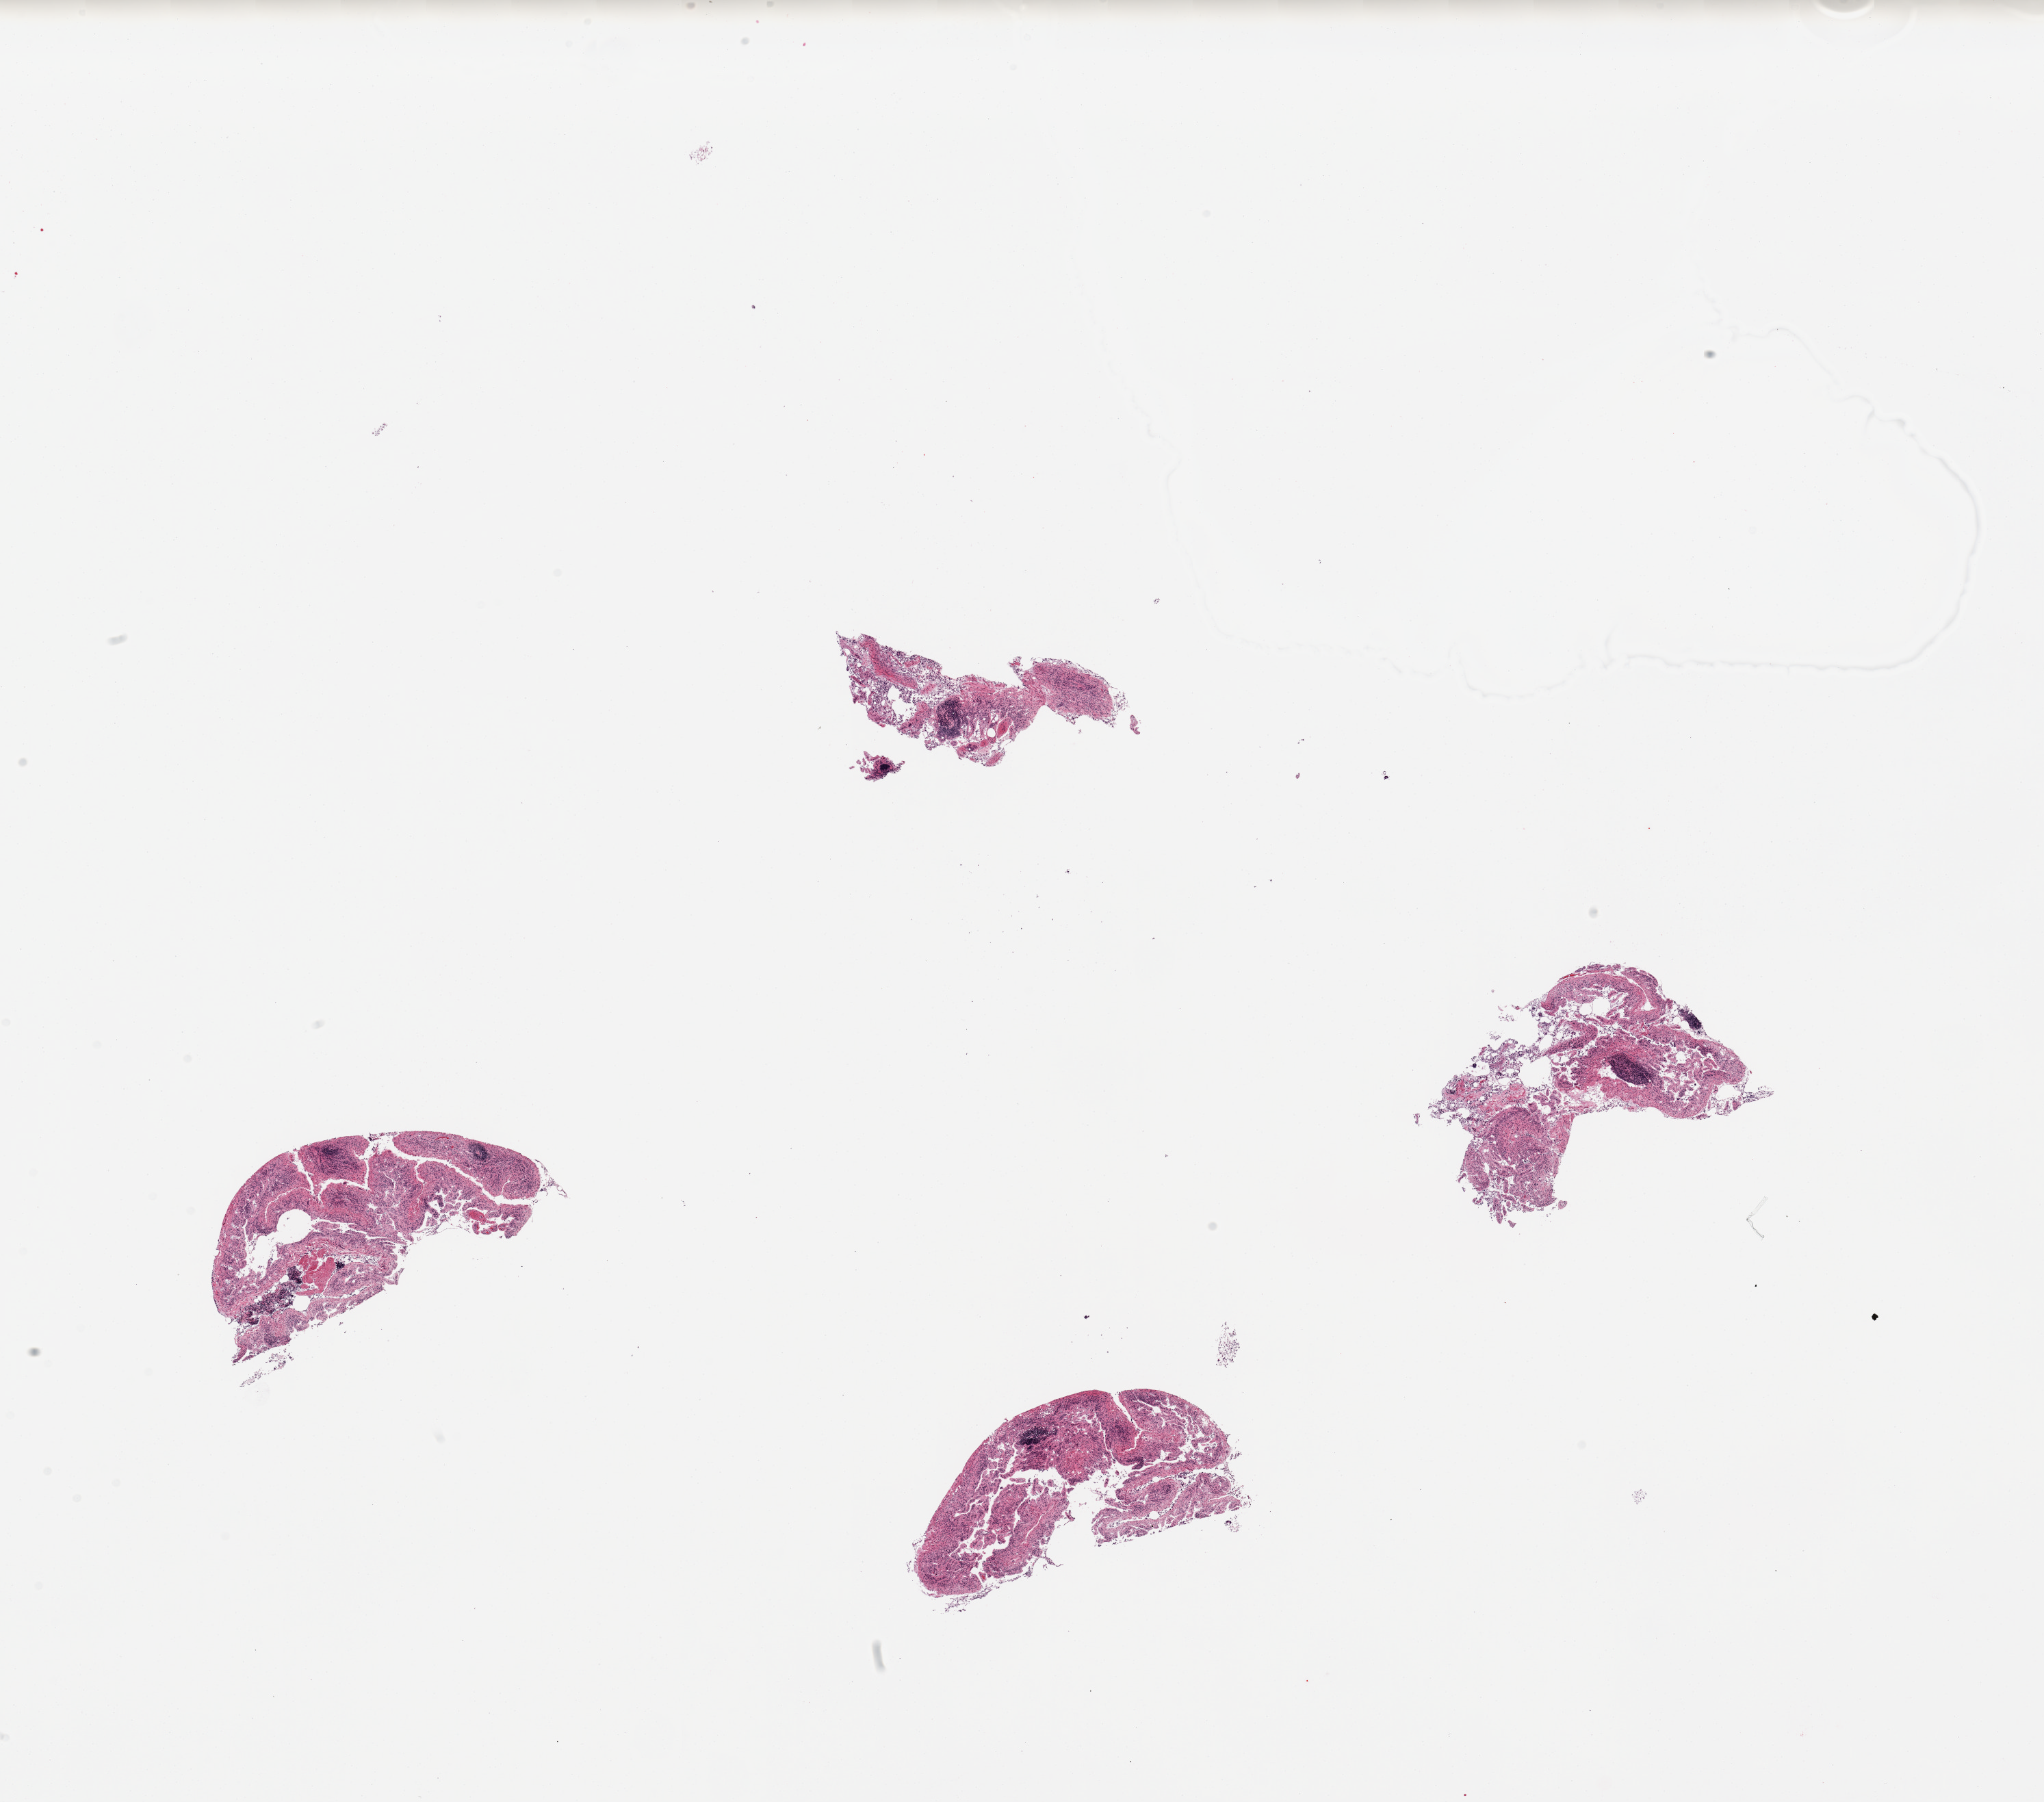
Digitized H&E-stained section, brightfield — a low-resolution overview of the entire scanned area, about 23.6 x 20.8 mm. Male donor.
Specimen: PAXgene-fixed paraffin-embedded (PFPE) section; section of ileum (target tissue); tissue donor sample.